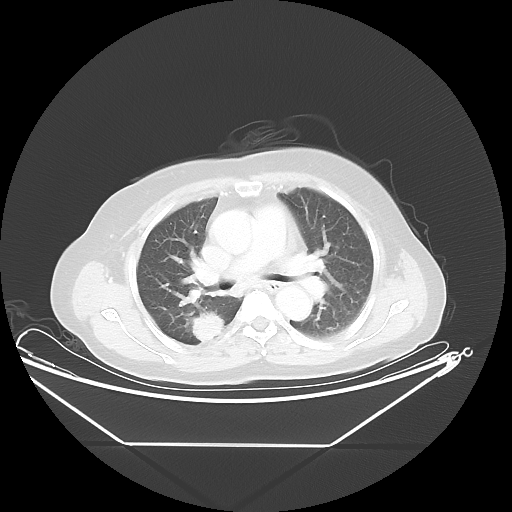
Chest CT, one axial slice; slice 29 of 48 in the series (ordered by position); 100 kVp; lung window (W 1500 / L -600 HU); 5 mm slice thickness; 512 × 512 image matrix, field of view 462 × 462 mm. Patient: female, 62 years. Case-level facts recorded for this patient, not image findings: clinical TNM (as recorded): T1c N0 M0.
Outlined on this slice (rectangle marked by the reading radiologist):
- lung tumour (recorded histology: adenocarcinoma): box from (x=181, y=305) to (x=232, y=349) px